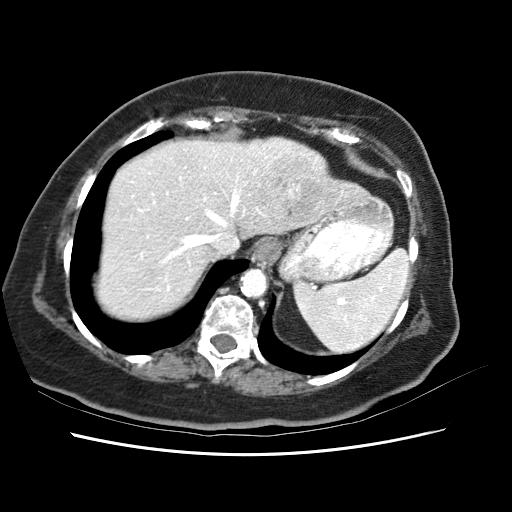
Contrast-enhanced abdominal CT (liver protocol), one axial slice. Position 50 of 62 along the scan axis. Reconstruction kernel STANDARD. 120 kVp. Soft-tissue window (W 400 / L 40 HU). 512 × 512 image matrix, field of view 340 × 340 mm. From the clinical record (not read from this slice): diagnosis: hepatocellular carcinoma (patient treated with transarterial chemoembolisation; whether this scan precedes or follows treatment is not stated here); TNM stage (as recorded): Stage-I; Child-Pugh class: B.
Outlined on this slice (semi-automatically segmented with operator editing):
- abdominal aorta: box from (x=241, y=270) to (x=266, y=296) px
- liver parenchyma outside the tumour (the mass and vessels are separate outlines, so this box may not span the whole liver): (x=110, y=138)–(x=347, y=306)
- mass: (x=260, y=150)–(x=323, y=217)
- liver vessels: (x=125, y=157)–(x=276, y=285)